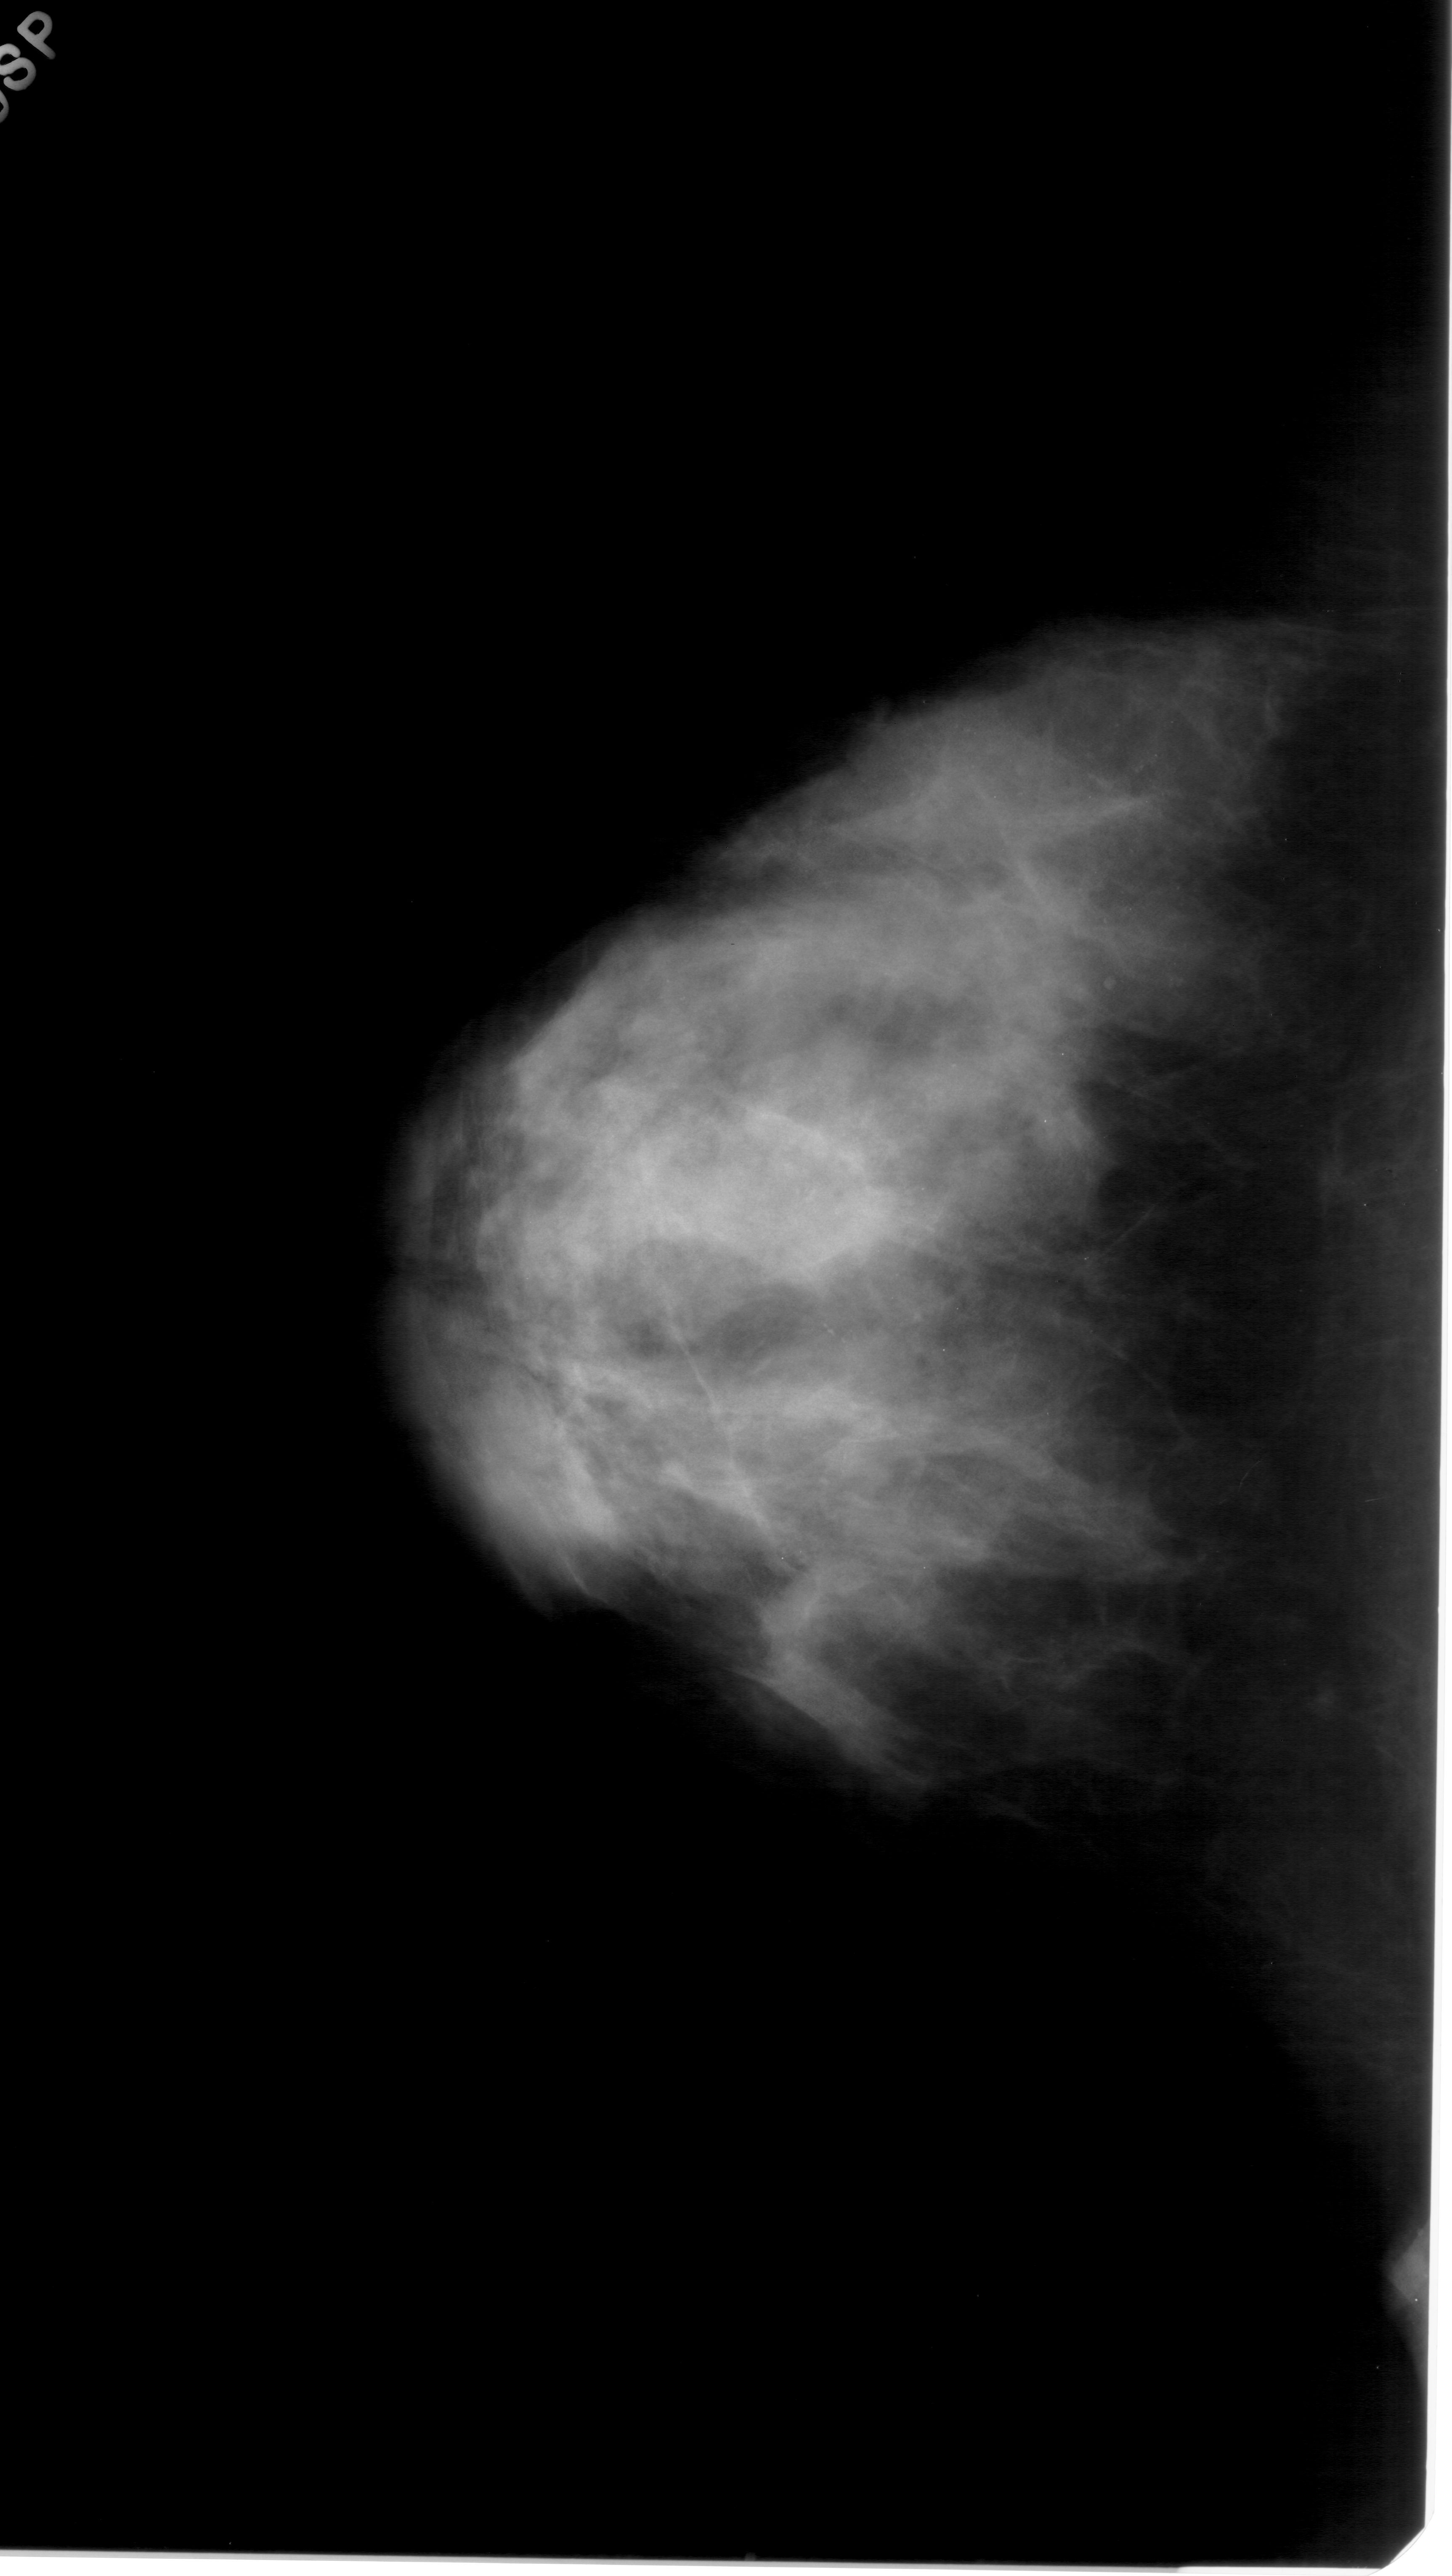
Mammogram (digitized film); left breast; craniocaudal (CC) view; BI-RADS breast density category 4 (scale 1–4).
Calcifications, morphology pleomorphic, distribution clustered; BI-RADS assessment category 4; subtlety rating 2 on a 1 (subtle) to 5 (obvious) scale; pathology (as recorded): benign.